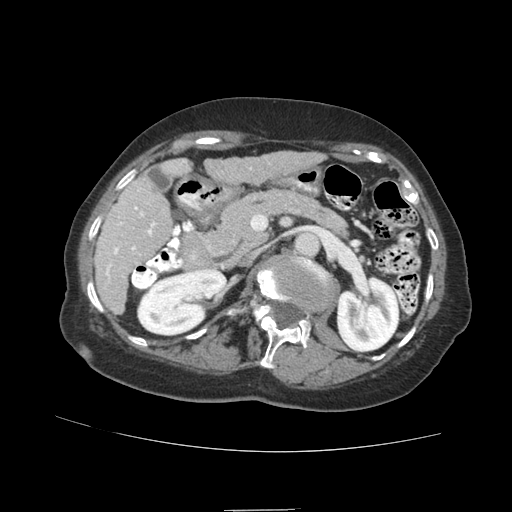
Contrast-enhanced abdominal CT (liver protocol), one axial slice. Position 36 of 89 along the scan axis. Reconstruction kernel STANDARD. 140 kVp. Soft-tissue window (W 400 / L 40 HU). 2.5 mm slice thickness. 512 × 512 image matrix, field of view 360 × 360 mm. Case-level facts recorded for this patient, not image findings: diagnosis: hepatocellular carcinoma (patient treated with transarterial chemoembolisation; whether this scan precedes or follows treatment is not stated here); TNM stage (as recorded): Stage-II; Child-Pugh class: A; tumour size: 4 cm.
Annotated regions visible in this slice (semi-automatically segmented with operator editing):
- liver parenchyma outside the tumour (the mass and vessels are separate outlines, so this box may not span the whole liver): bounding box [x1, y1, x2, y2] px = [94, 150, 323, 314]
- liver vessels: [106, 161, 184, 276]